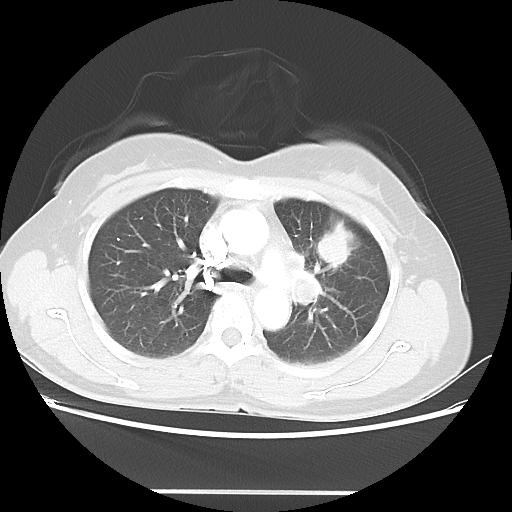
Chest CT, one axial slice. Reconstruction kernel LUNG. Lung window (W 1500 / L -600 HU). 5 mm slice thickness. 512 × 512 image matrix, field of view 360 × 360 mm. Female patient, age 50 years. From the clinical record (not read from this slice): clinical TNM (as recorded): T1c N1 M0; histopathological grade: G3.
Structures marked on this image (bounding box drawn by a radiologist):
- lung tumour (recorded histology: adenocarcinoma): bounding box (x1, y1, x2, y2) in pixels: (312, 217, 357, 268)